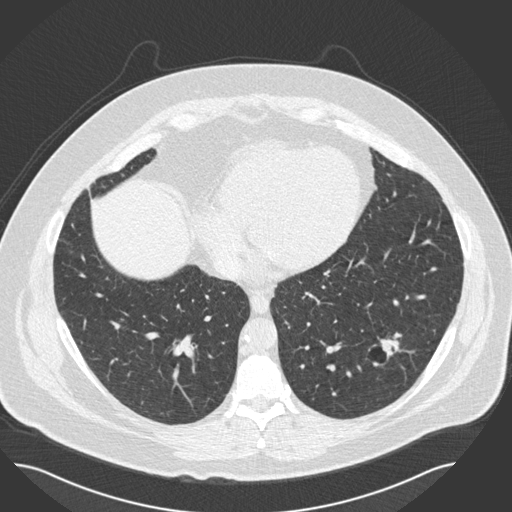
Axial slice from a low-dose chest CT screening exam; second screening round (one year after baseline); lung window (W 1500 / L -600 HU); 2 mm slice thickness; slice 93 of 162 in the series; 512 × 512 image matrix, field of view 422 × 422 mm. Male participant, aged 57 years at enrolment. Current smoker at enrolment.
• Lesion marked by an expert reader, bounding box [x1, y1, x2, y2] px = [354, 324, 420, 379].
• Reader record for this screening exam (exam-level; its link to the box is not recorded): non-calcified nodule or mass ≥4 mm, left lower lobe, 19 × 15 mm, pre-existing on the prior screen: yes; interval growth: no.
• Official screen result: positive, no significant change: stable abnormalities potentially related to lung cancer, unchanged since the prior screening exam.
• Later outcome: lung cancer diagnosed 434 days after this screen — squamous cell carcinoma, NOS, left lower lobe, moderately differentiated (G2), stage IA (AJCC 6th edition), 22 mm at pathology.